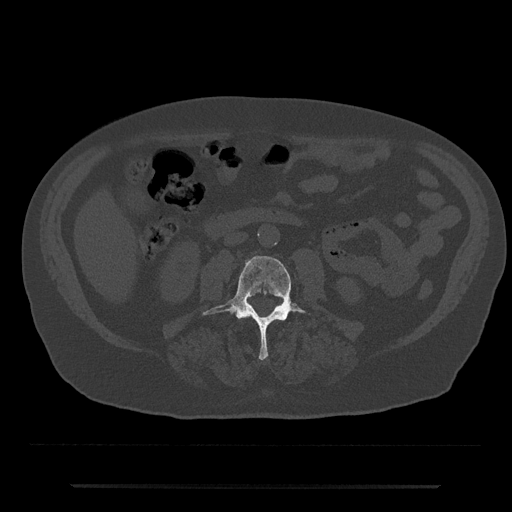
CT including the spine, one axial slice; position 410 of 797 along the scan axis; 120 kVp; bone window (W 1800 / L 400 HU); 0.5 mm slice thickness; 512 × 512 image matrix, field of view 434 × 434 mm. Male patient, age 80 years. From the clinical record (not read from this slice): primary cancer: prostate.
Structures marked on this image (semi-automatic segmentation, software-assisted and operator-edited):
- L3 vertebra: bounding box [x1, y1, x2, y2] px = [204, 256, 304, 360]